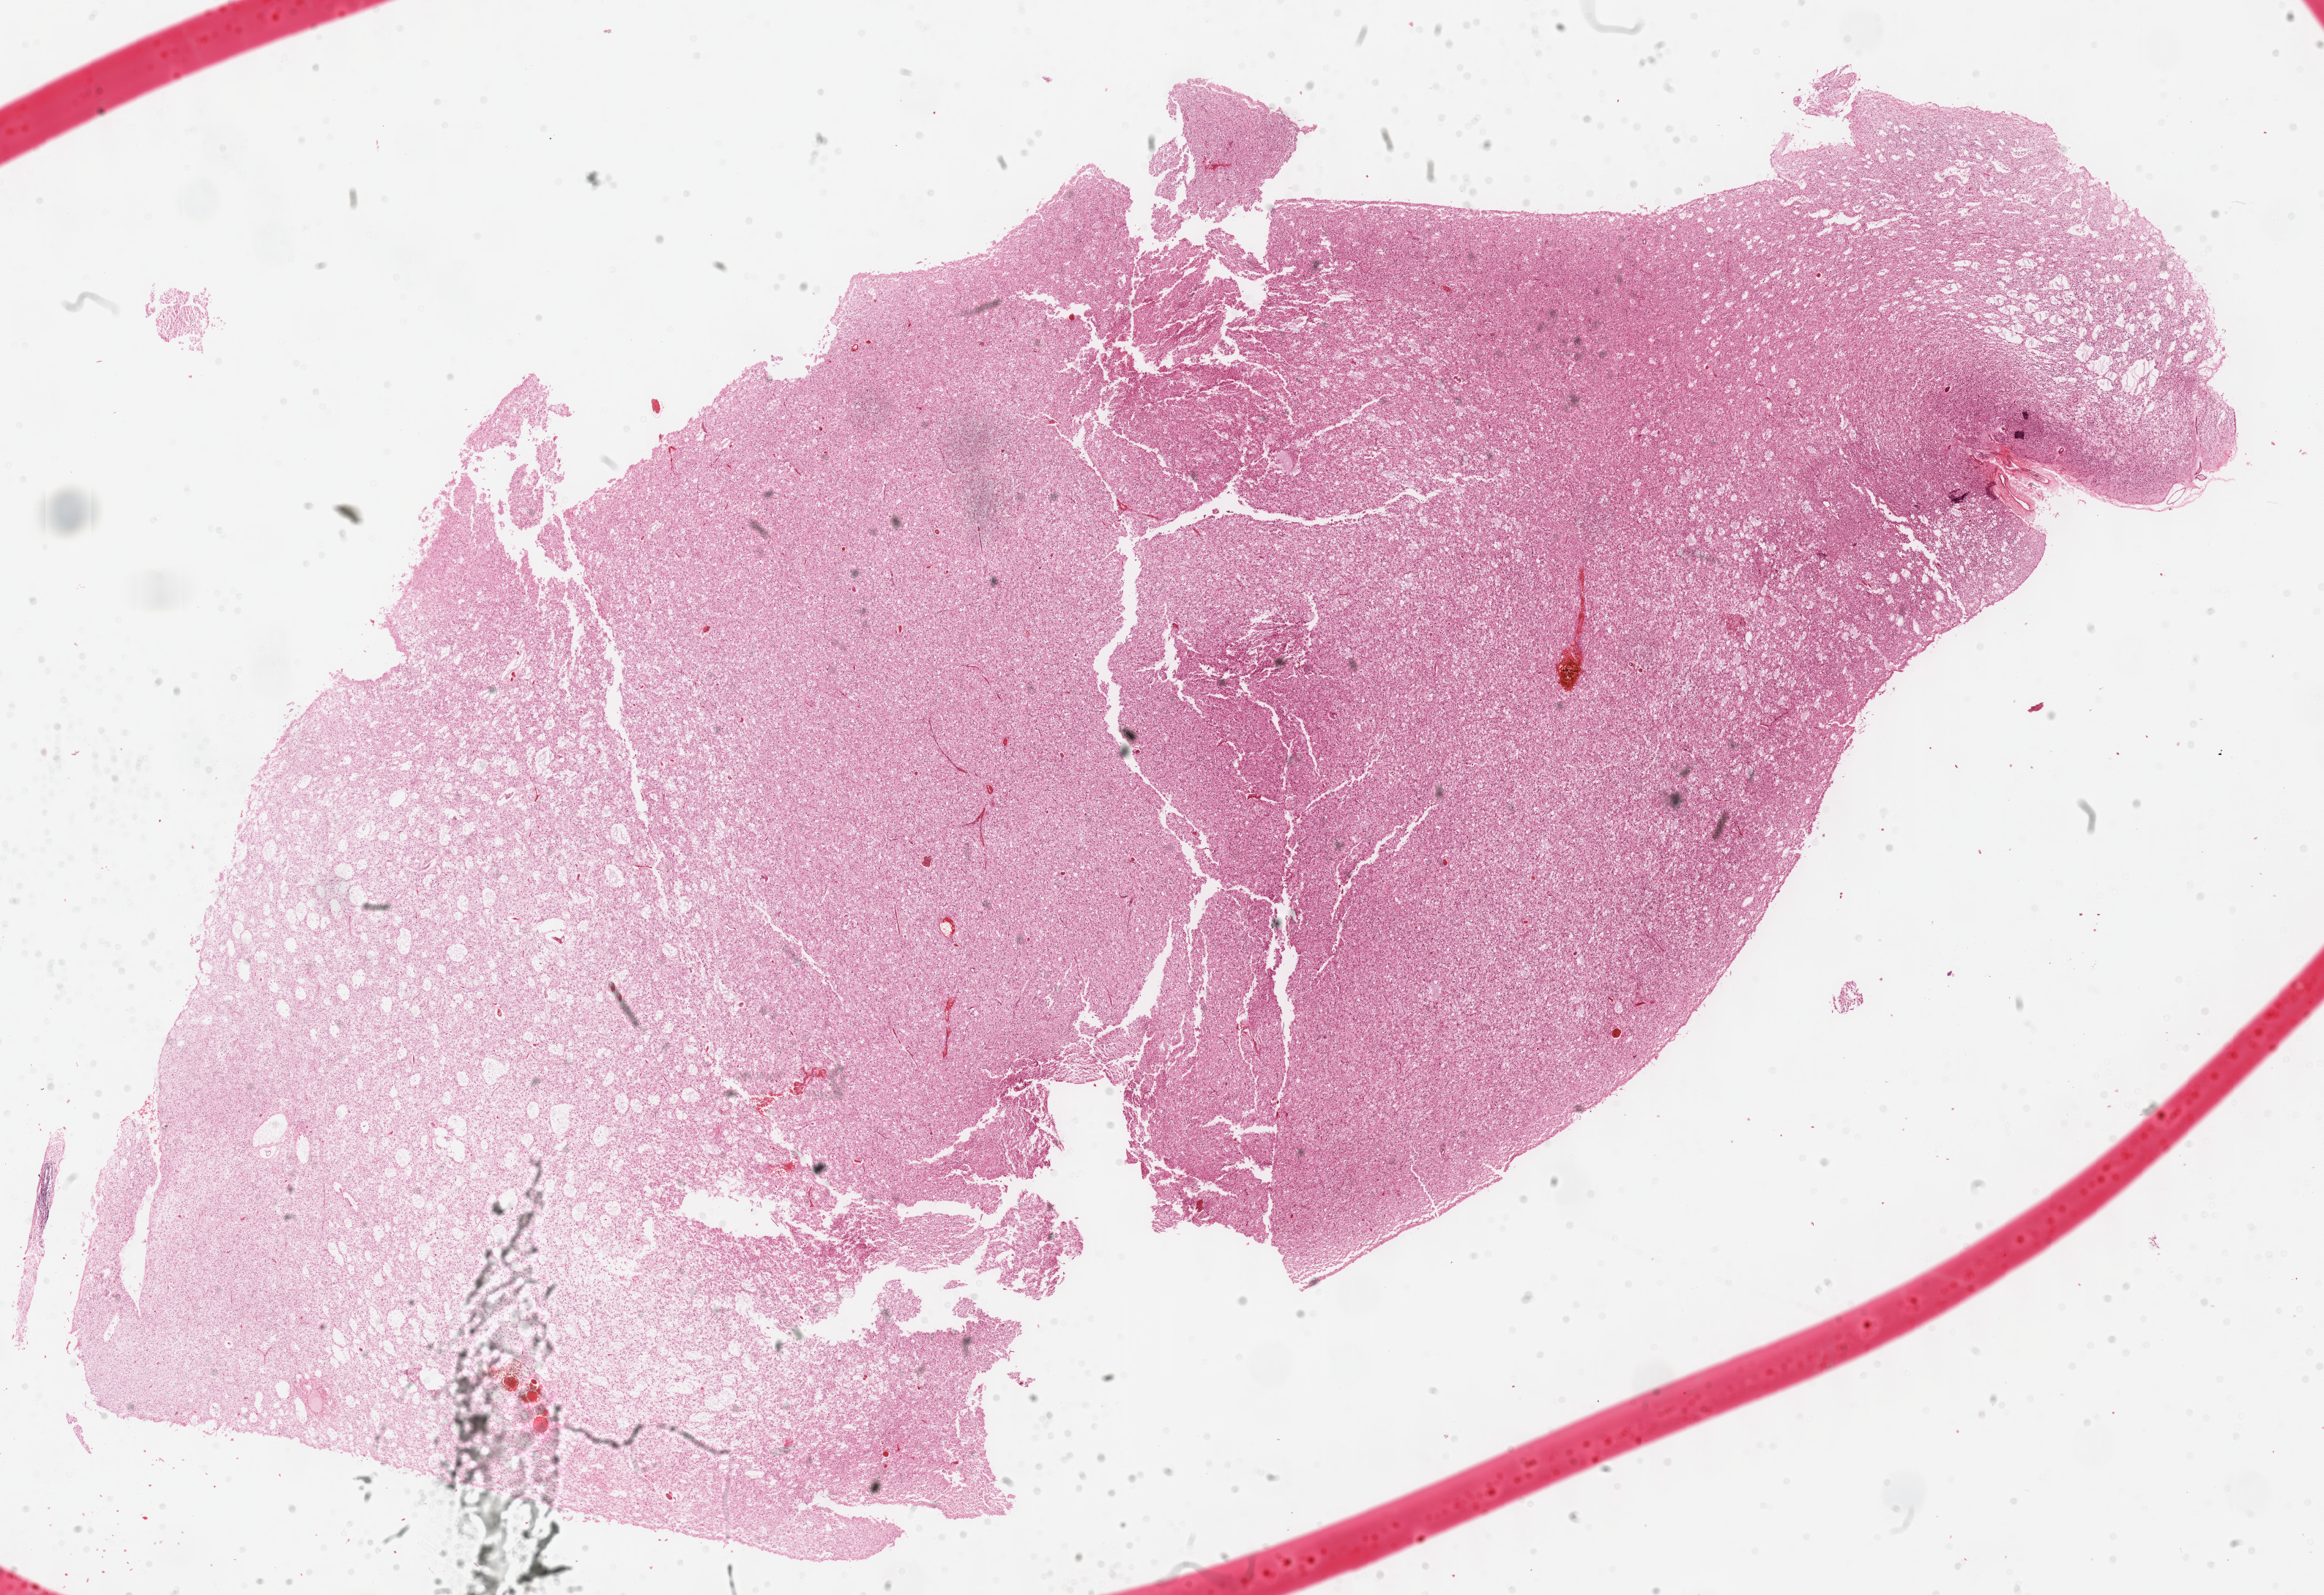
Digitized H&E-stained tissue section (whole slide) — low-resolution overview of the scanned area, about 25.7 x 17.6 mm (acquisition: 40x scan); formalin-fixed paraffin-embedded (FFPE) diagnostic section; sample: primary tumour, brain. Male patient; age at initial diagnosis 44 years. Histologic grade: G2 (moderately differentiated).
Pathologic diagnosis: Astrocytoma, NOS. Laterality: left.